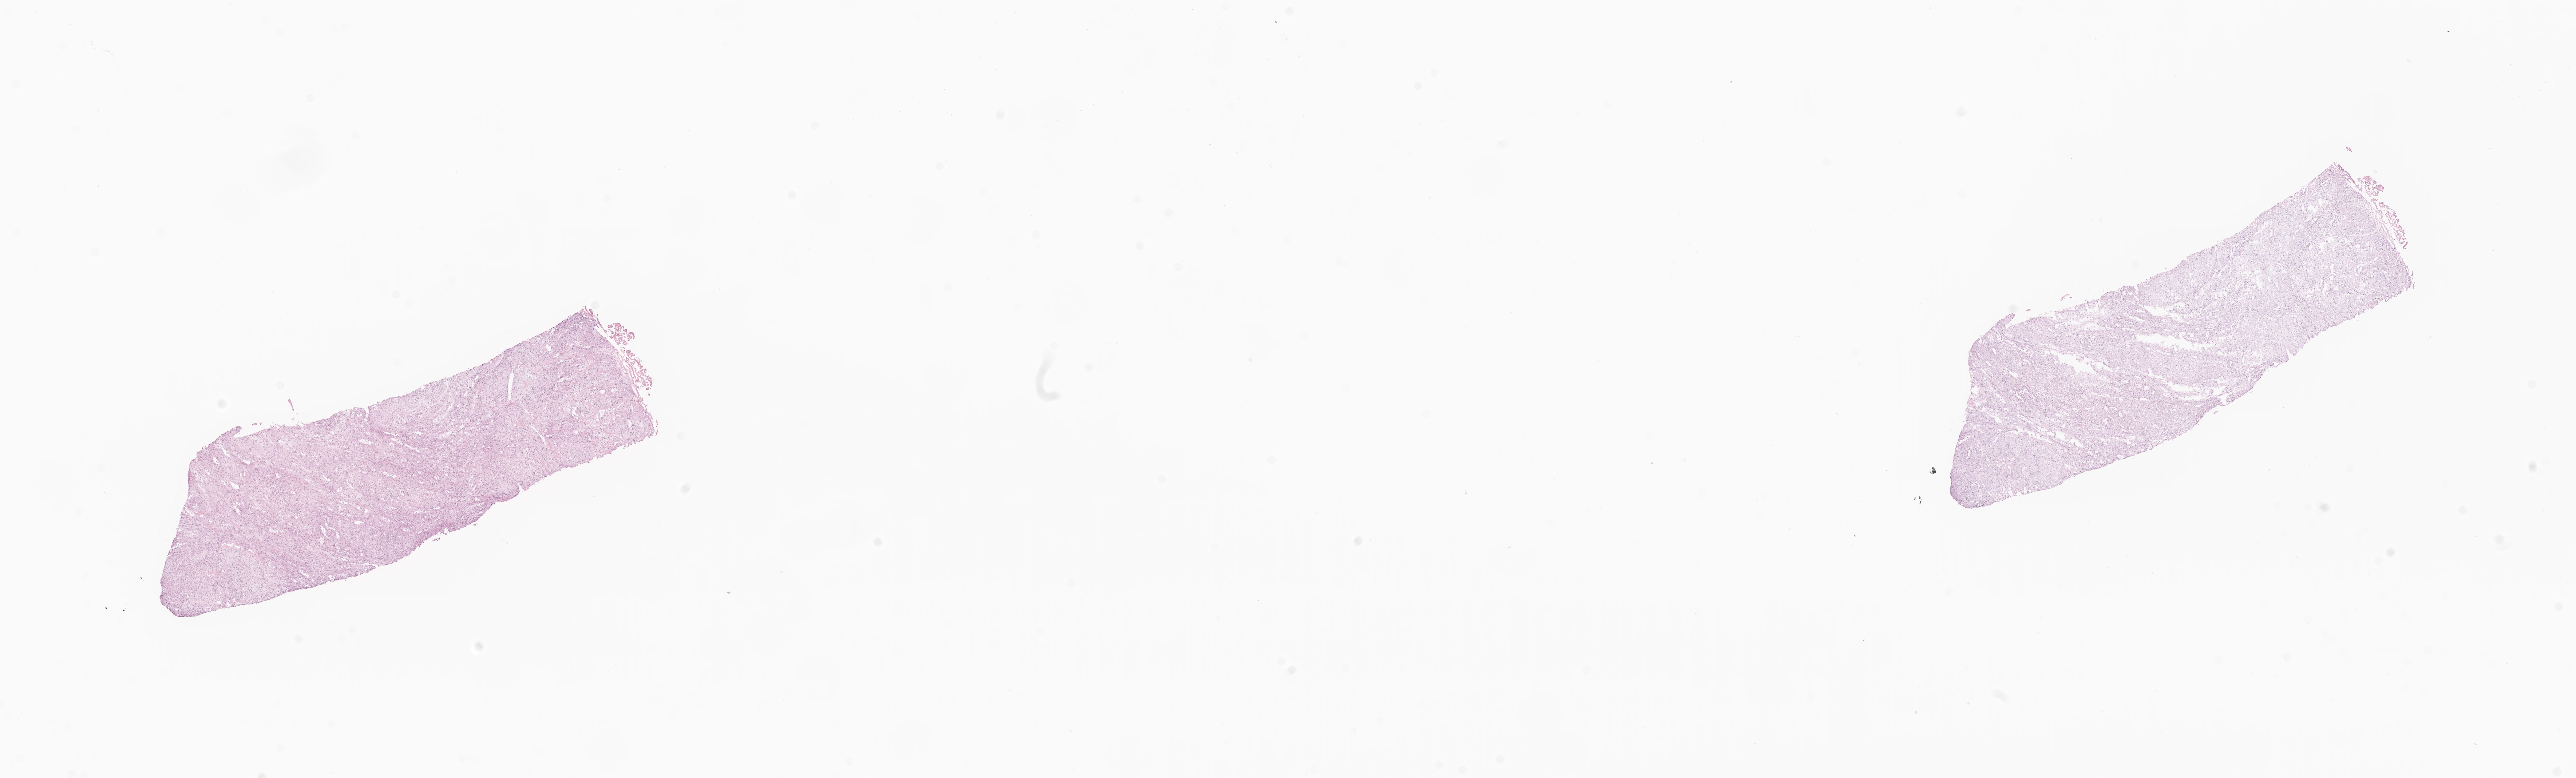
Whole-slide image, H&E stain of tumor tissue from the cranial and/or facial bone, low-resolution overview of the scanned area, about 29.8 x 9.0 mm. Cryosection (OCT / tissue freezing medium). Patient: male, age 48 months (4 years).
Diagnosis (ICD-O-3 morphology term): Myofibroma. Tissue or organ of origin (case record): bones of skull and face and associated joints.